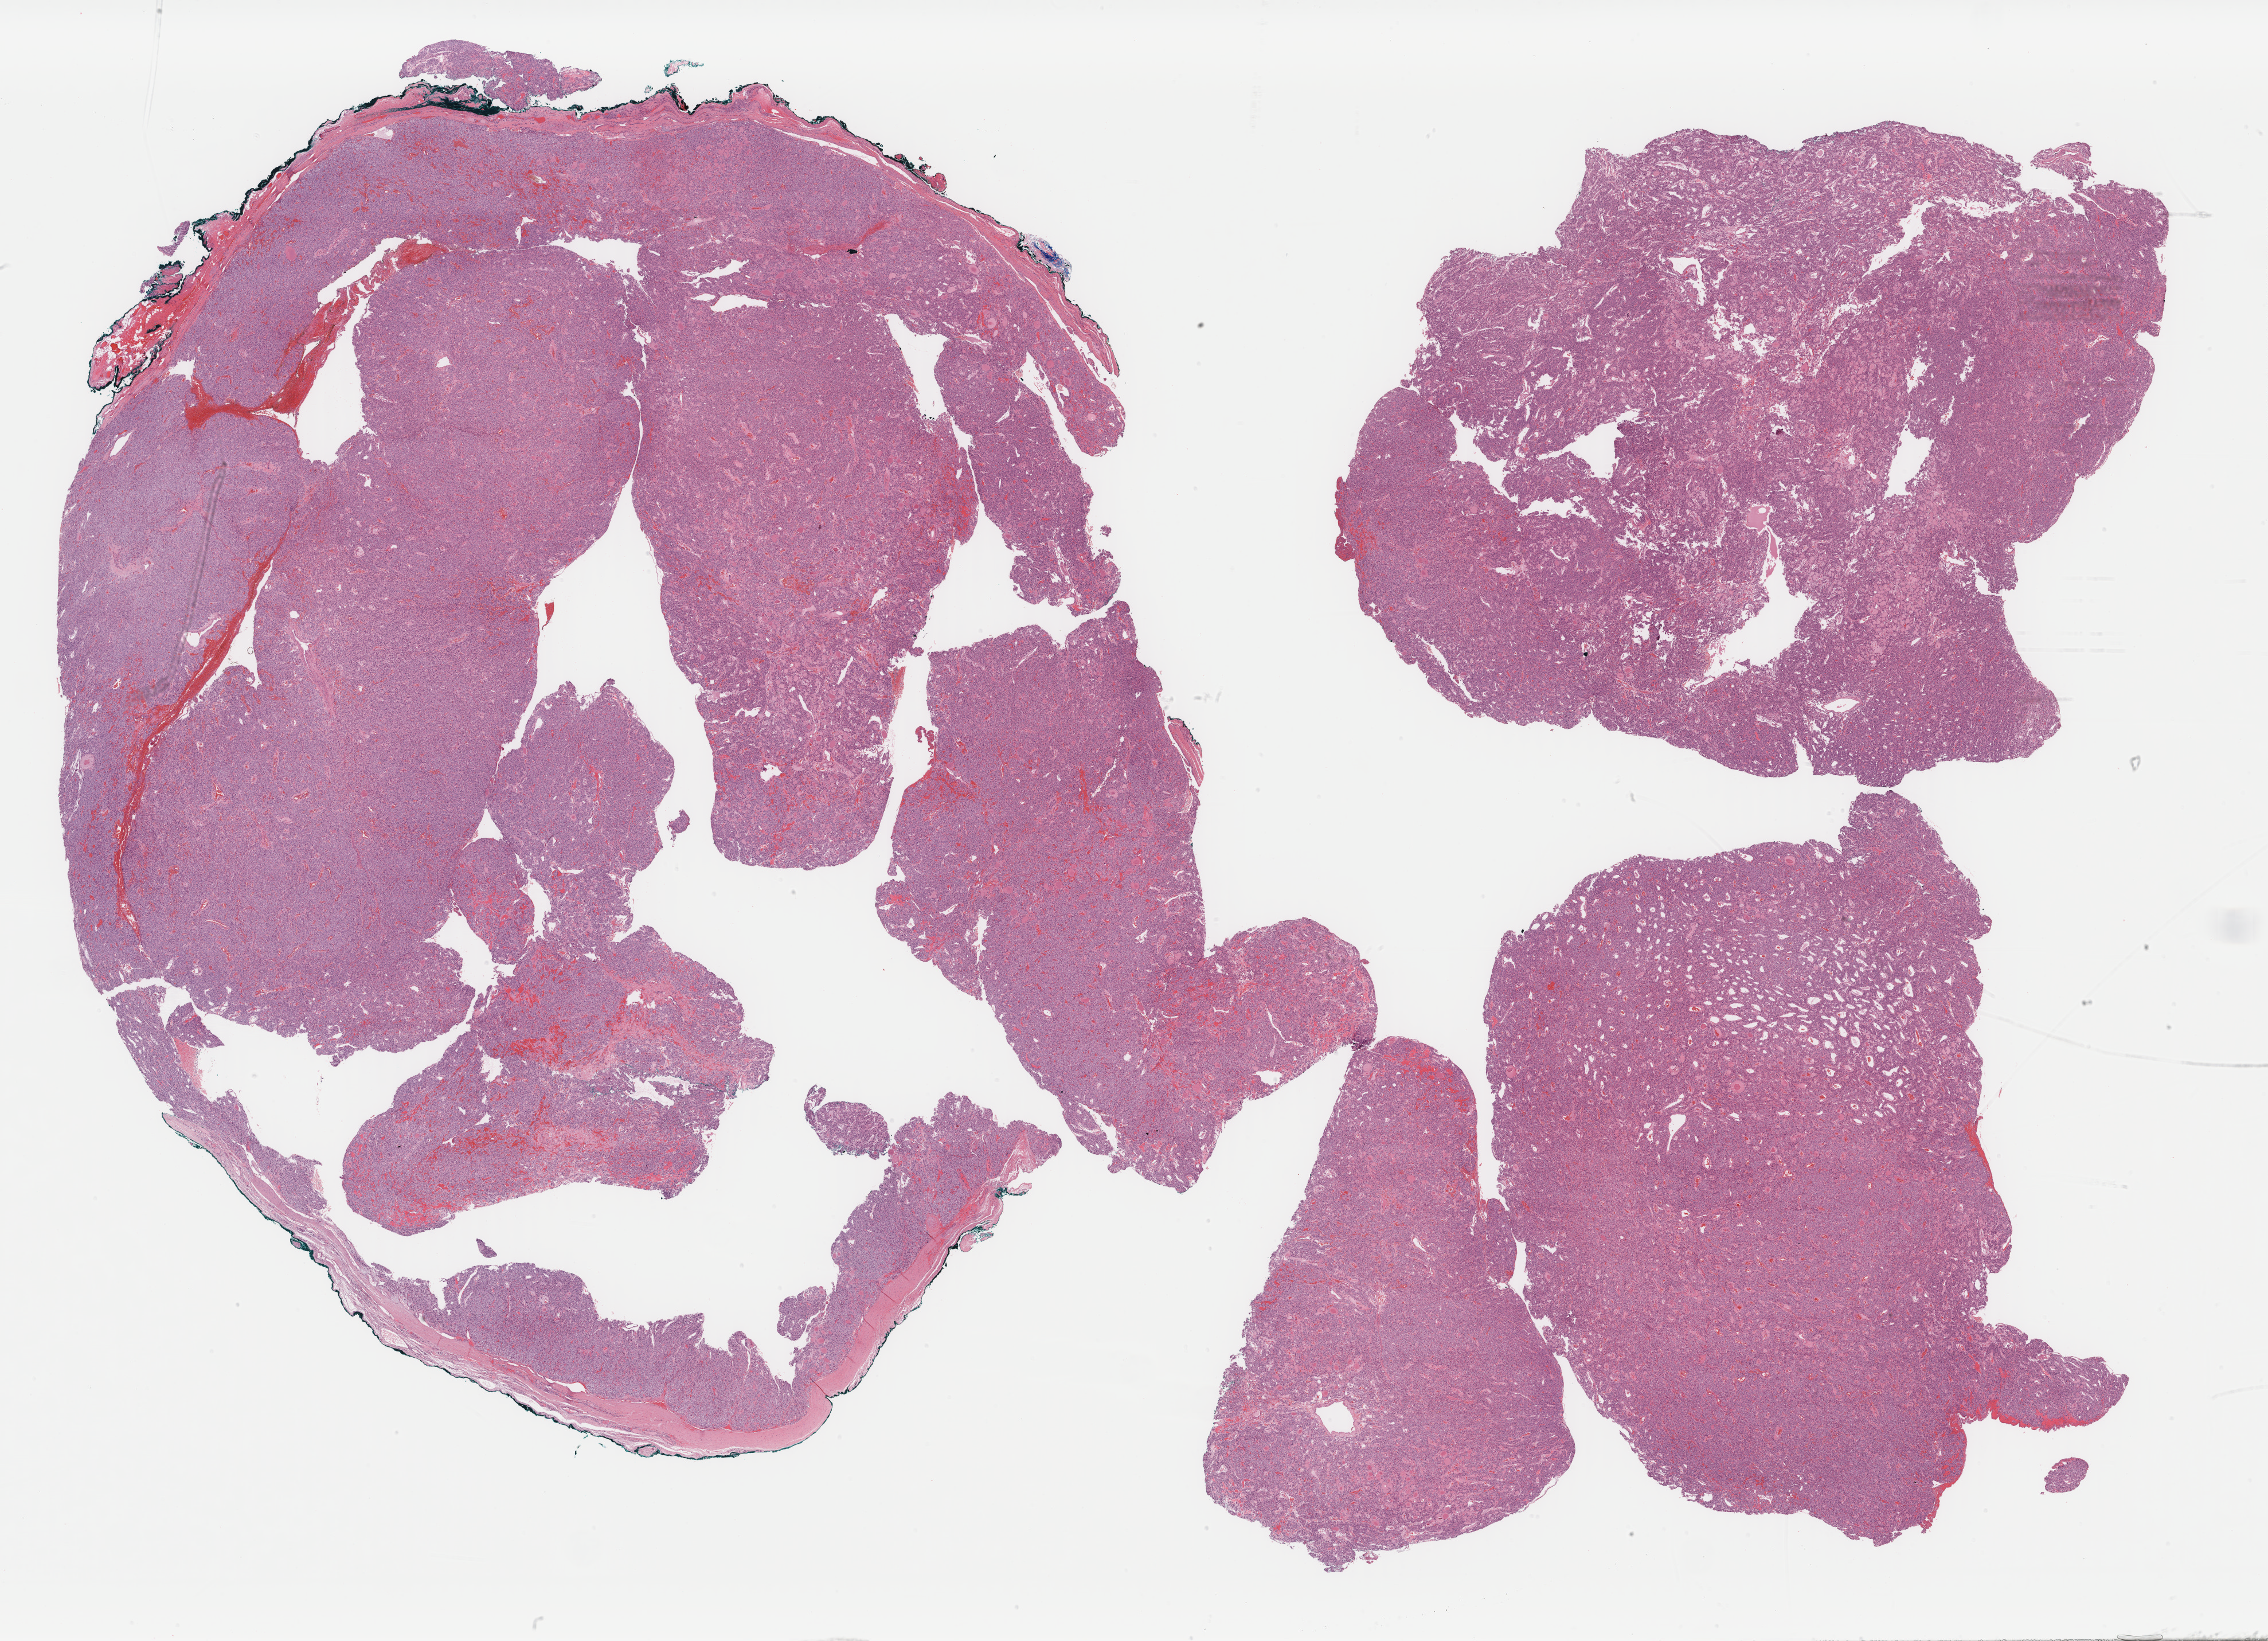
Whole-slide histology image, Hematoxylin and eosin (H&E) stained, low-resolution overview of the scanned area, about 31.4 x 22.7 mm (from a 40x scan). FFPE section. Sample: primary tumour, thyroid. Female, age 39 years at initial diagnosis.
• diagnosis: Papillary carcinoma, follicular variant
• lymph nodes positive (case pathology): 0 of 3 examined
• AJCC pathologic stage: I (6th edition)